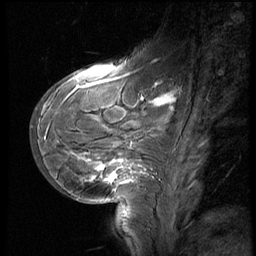
Breast MRI (dynamic contrast-enhanced), one sagittal slice. Slice 20 of 60 in the series (ordered by position). 3 images stored at this slice position (order not interpretable as contrast timing). 1.5 T. TE 4.2 ms, TR 8.9 ms. 2.5 mm slice thickness. 256 × 256 image matrix, field of view 200 × 200 mm. Female patient, age 29 years. Case-level facts recorded for this patient, not image findings: setting: breast cancer imaged before/during neoadjuvant chemotherapy.
Outlined on this slice (semi-automatic segmentation, software-assisted and operator-edited):
- analysis volume of interest (the breast-tissue region the enhancement analysis was run in; not a lesion): bounding box (x1, y1, x2, y2) in pixels: (32, 57, 185, 200)
- tumour enhancement mask (voxels above the 140 % enhancement threshold inside the analysis volume of interest): (46, 87, 173, 184)